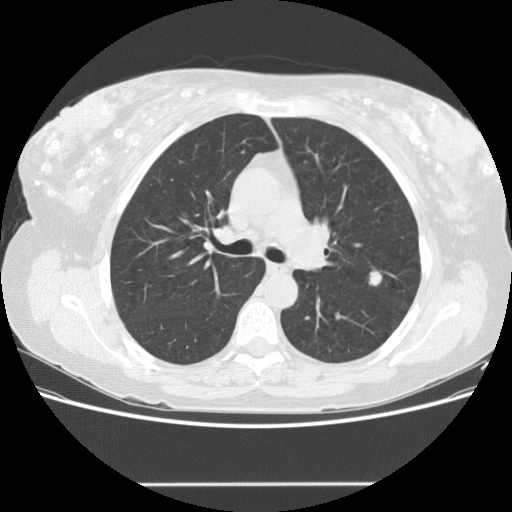
Low-dose screening chest CT, one axial slice; position 98 of 151 along the scan axis; 120 kVp; lung window (W 1500 / L -600 HU); 2.5 mm slice thickness; 512 × 512 image matrix, field of view 360 × 360 mm.
Annotated regions visible in this slice (expert manual segmentation):
- lesion 1 (tumor, upper lobe of left lung): bounding box (x1, y1, x2, y2) in pixels: (369, 270, 382, 286)